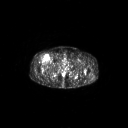
FDG PET of an extremity soft-tissue mass (from a PET/CT study), one axial slice. Position 306 of 311 along the scan axis. 3.27 mm slice thickness. 128 × 128 image matrix, field of view 700 × 700 mm. Male patient, age 56 years. Case-level facts recorded for this patient, not image findings: histological type: pleiomorphic leiomyosarcoma; grade: intermediate; site of the primary tumour: right thigh.
Outlined on this slice (expert contour drawn on MRI and transferred to this co-registered scan by the dataset authors):
- gross tumour volume including surrounding oedema: bounding box (x1, y1, x2, y2) in pixels: (43, 54, 50, 62)
- gross tumour volume (mass): (46, 57, 50, 62)